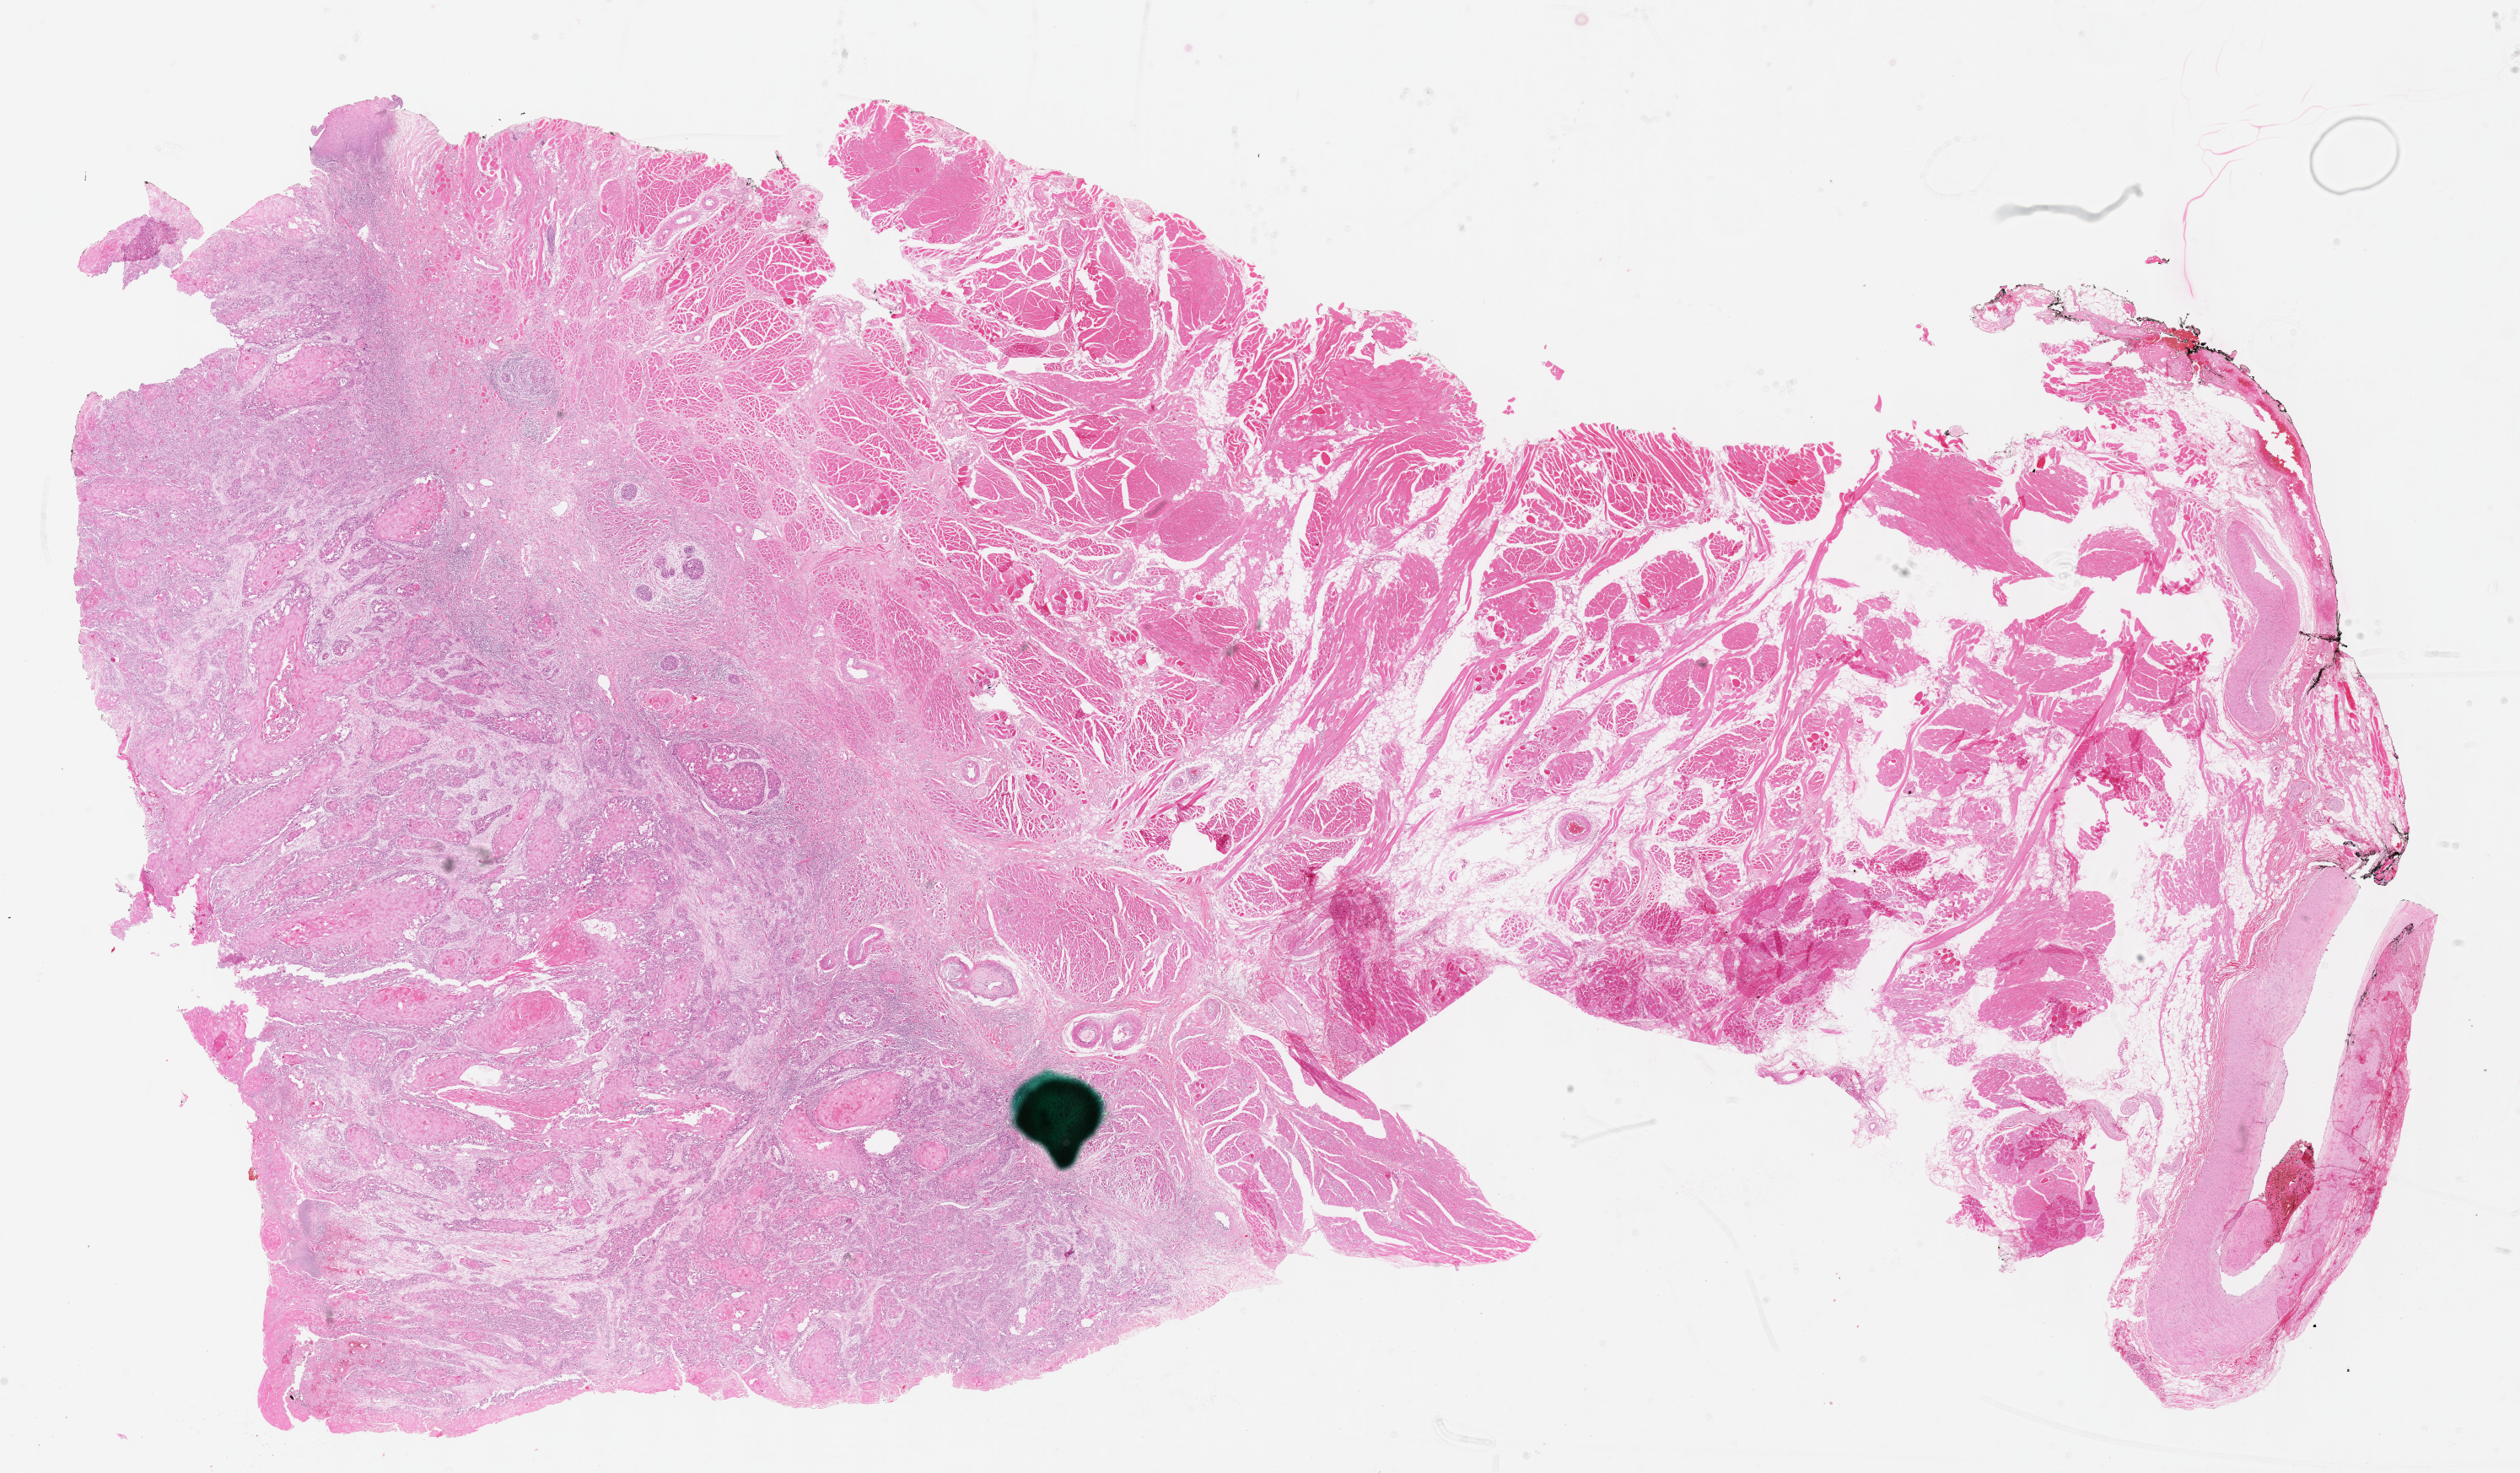
Digitized H&E-stained tissue section (whole slide) — shown as a low-resolution overview of the whole scanned area (about 24.1 x 14.1 mm, acquisition: 40x scan); formalin-fixed paraffin-embedded (FFPE) diagnostic section; sample: primary tumour, head and neck. Male, age 65 years at initial diagnosis. Histologic grade: G1 (well differentiated).
* AJCC pathologic stage: II (7th edition)
* pathologic diagnosis: Squamous cell carcinoma, NOS (overlapping lesion of lip, oral cavity and pharynx)
* laterality: right